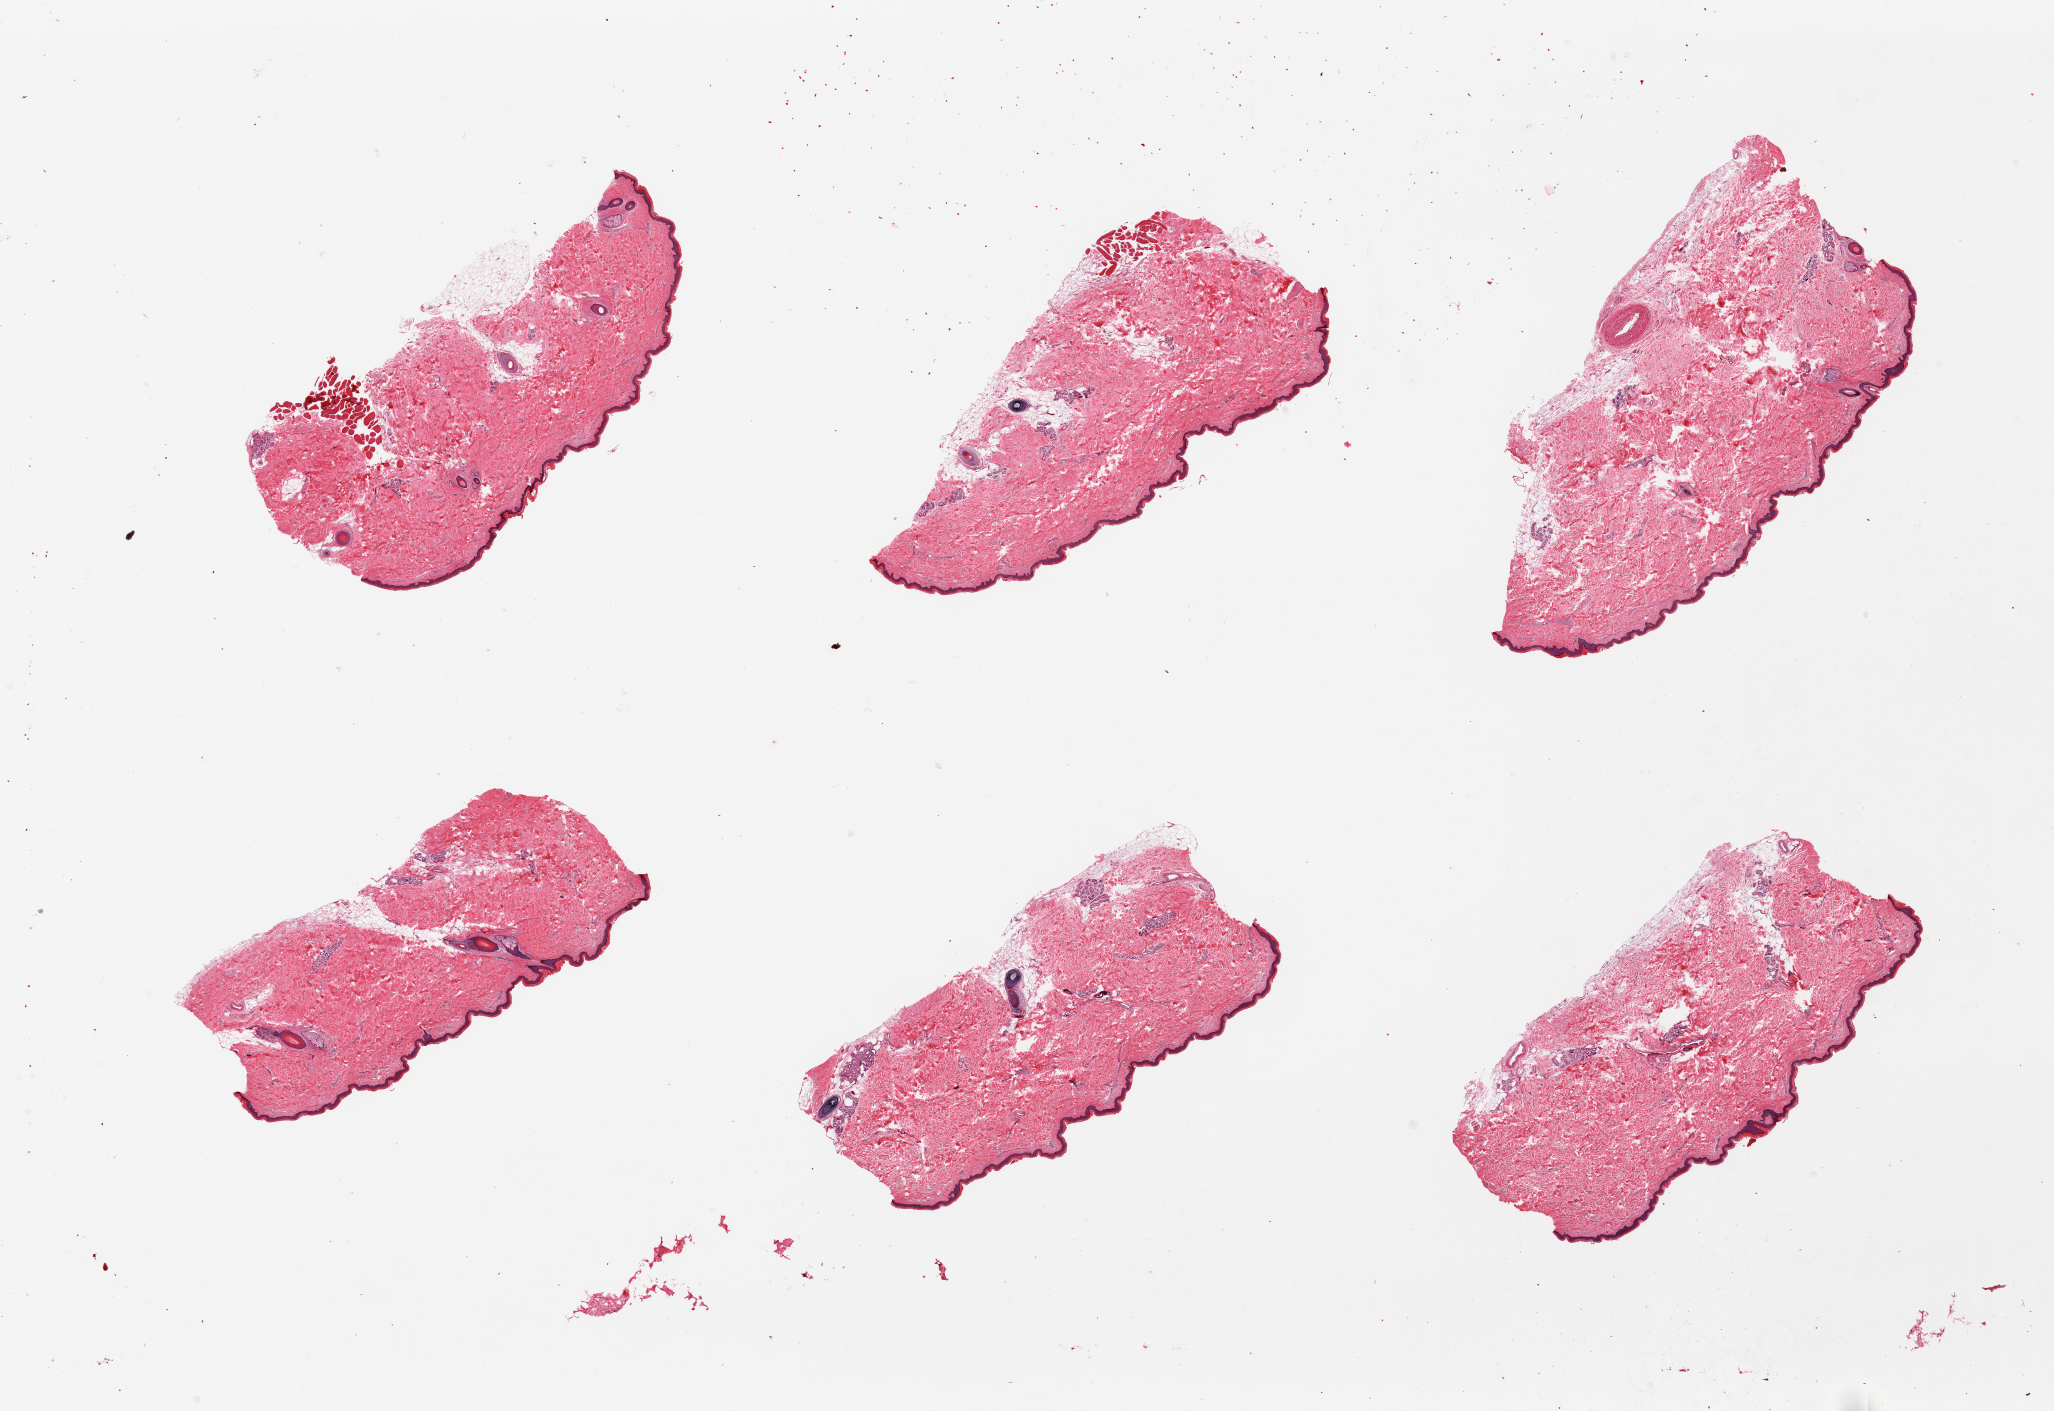
Whole-slide image, haematoxylin and eosin stain, low-resolution overview of the scanned area, about 32.5 x 22.3 mm; PAXgene-fixed, paraffin-embedded tissue; section of skin of lower leg (target tissue); tissue donor sample. Male donor.
Pathologist's review note for this sample: 6 pieces. Squamous epithelium is ~1.5-2% thickness; minimal dermal fat.